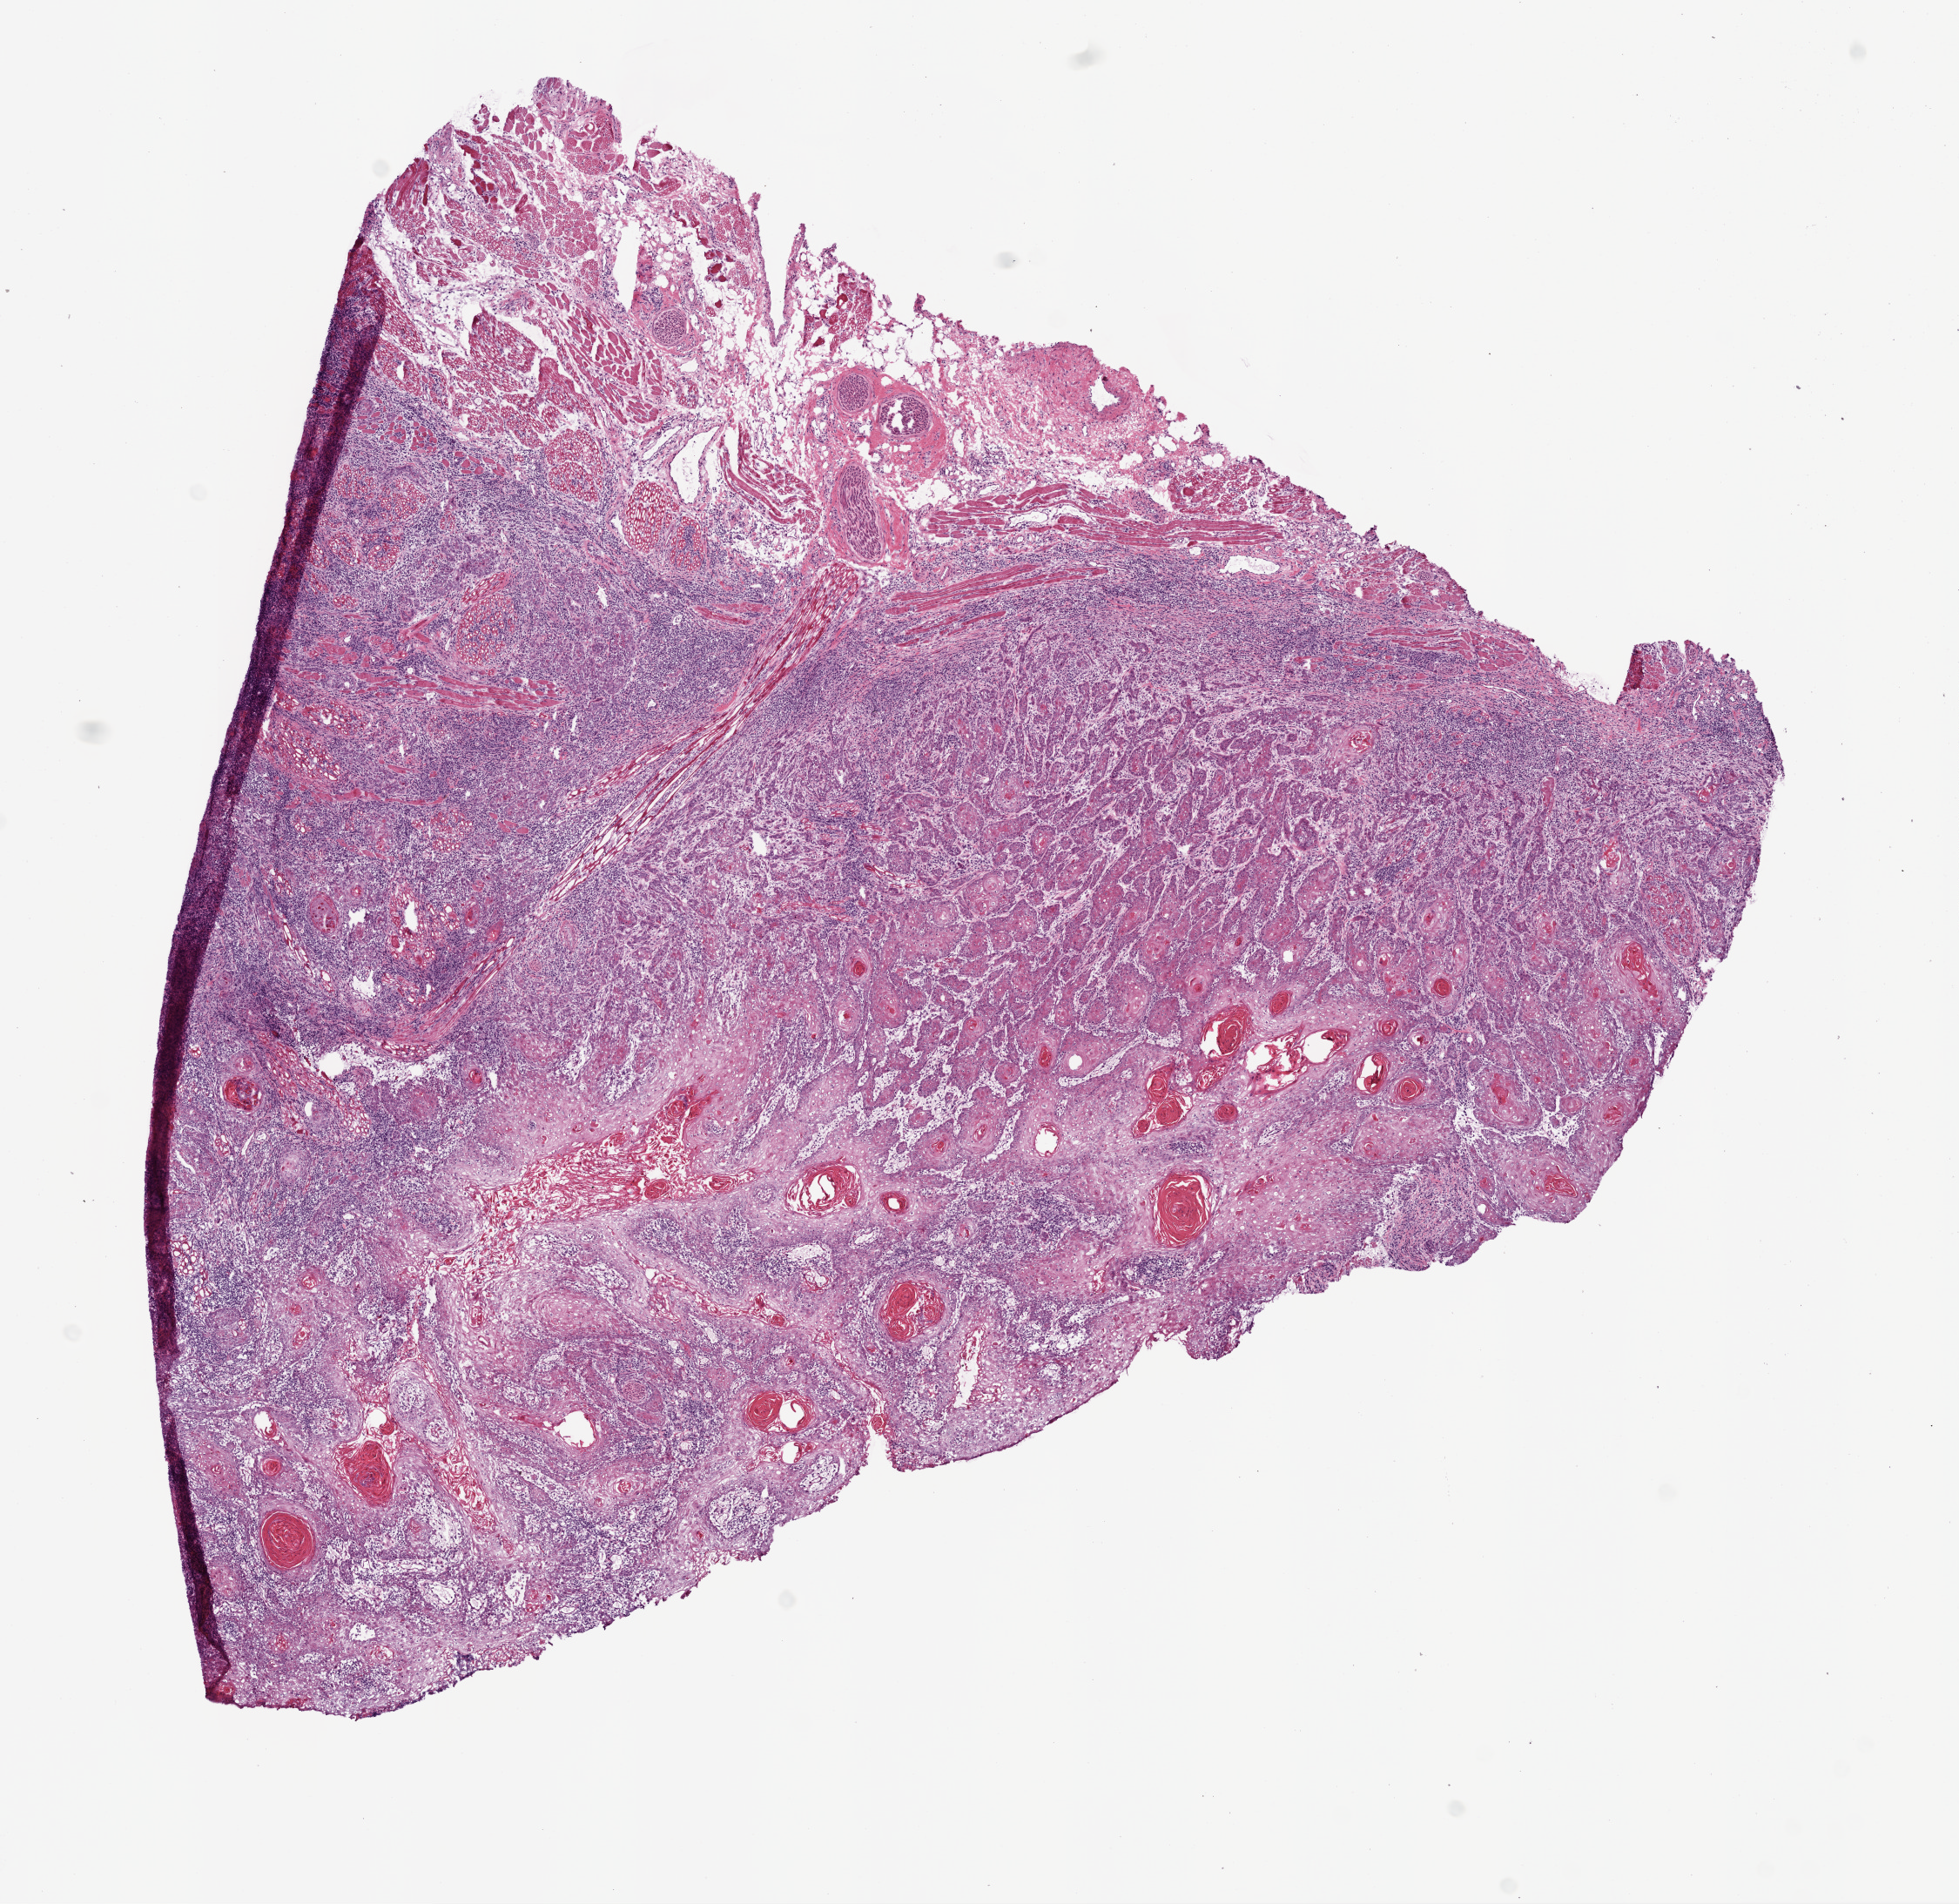
Digitized Hematoxylin and eosin (H&E) stained tissue section (whole slide) — shown as a low-resolution overview of the whole scanned area (about 9.0 x 8.8 mm), frozen section from the bottom of the tissue portion, sample: primary tumour, head and neck. Male, age 65 years at initial diagnosis. Histologic grade: G2 (moderately differentiated). Pathologist review of this section (percent, as recorded): tumour cells 80%, tumour nuclei 71%, normal cells 14%, necrosis 6%. Infiltration values recorded for this section: lymphocyte infiltration 25%, neutrophil infiltration 2%.
* laterality: left
* lymph nodes positive (case pathology): 0 of 22 examined
* diagnosis: Squamous cell carcinoma, NOS (tongue, NOS)
* AJCC pathologic stage: I (6th edition)